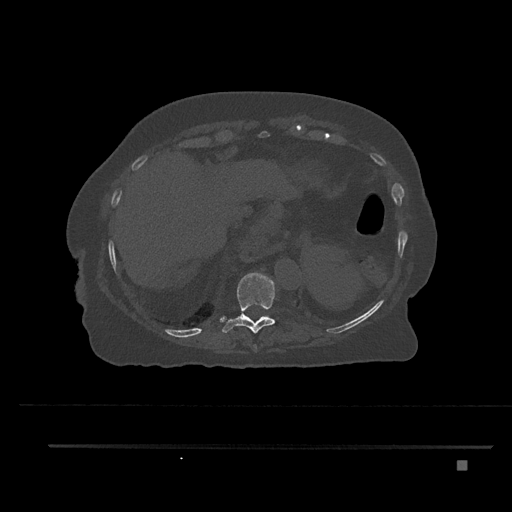
CT including the spine, one axial slice. Position 353 of 797 along the scan axis. Reconstruction kernel Br40s/3. Bone window (W 1800 / L 400 HU). 512 × 512 image matrix. Patient: female, 76 years. From the clinical record (not read from this slice): primary cancer: lung; vertebrae with lytic lesions (as recorded): T11, L3.
Structures marked on this image (semi-automatically segmented with operator editing):
- T10 vertebra: bounding box (x1, y1, x2, y2) in pixels: (220, 272, 276, 333)
- T11 vertebra: (245, 315, 247, 317)
- T9 vertebra: (253, 344, 257, 351)